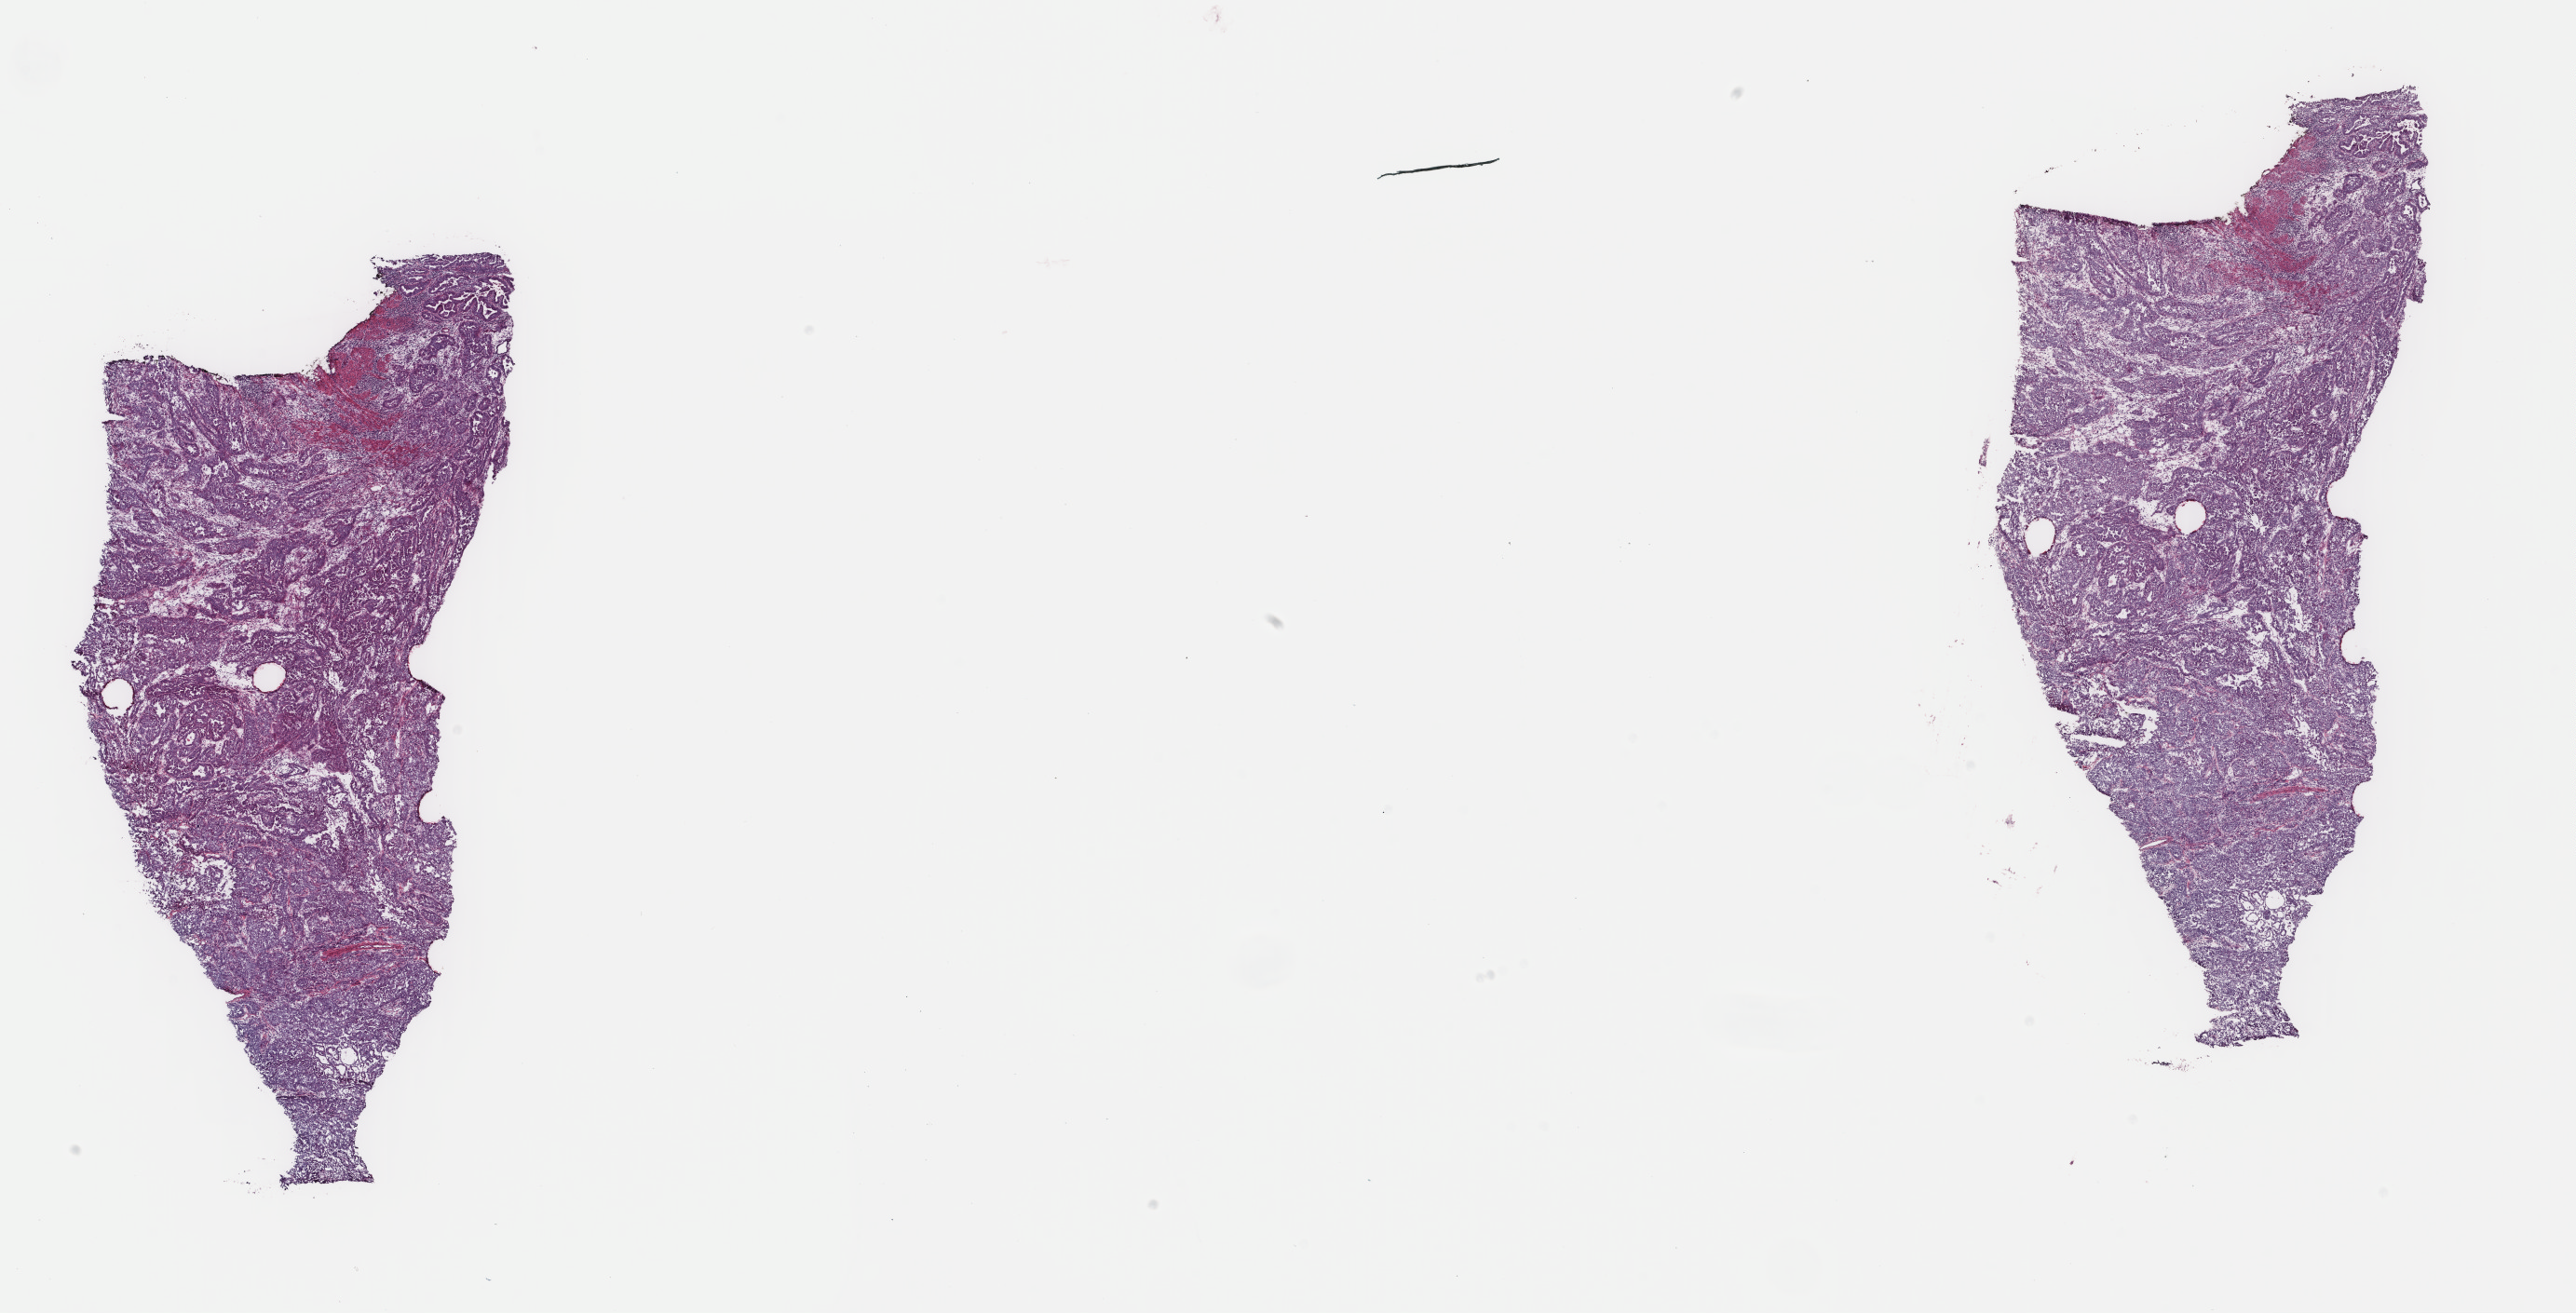
Whole-slide histology image, H&E-stained, low-resolution overview of the scanned area, about 22.0 x 11.2 mm (slide scanned at 40x); frozen section from the top of the tissue portion; uterus, primary tumour sample. Patient sex: female. Histologic grade: G3 (poorly differentiated). Slide review estimates, as recorded: tumour cells 90%, tumour nuclei 90%, normal cells 6%, stromal cells 2%, necrosis 2%. Infiltration values recorded for this section: lymphocyte infiltration 2%, monocyte infiltration 1%, neutrophil infiltration 0%.
Pathologic diagnosis: Endometrioid adenocarcinoma, NOS. FIGO stage: IB.